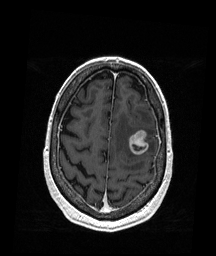
Brain MRI from a brain-tumour surgery series, one axial slice. Position 49 of 176 along the scan axis. T1-weighted post-contrast. 216 × 256 image matrix, field of view 211 × 250 mm. From the clinical record (not read from this slice): histopathology: Metastatic Melanoma.
Annotated regions visible in this slice (expert manual segmentation):
- tumour: bounding box [x1, y1, x2, y2] px = [128, 129, 149, 155]